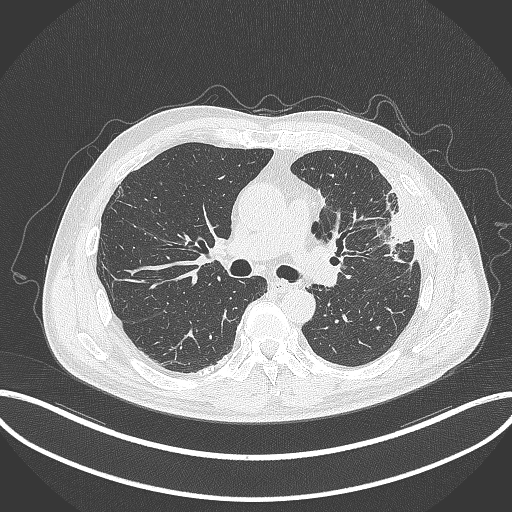
Chest CT, one axial slice. Slice 201 of 382 in the series (ordered by position). Reconstruction kernel B70f. 120 kVp. Lung window (W 1500 / L -600 HU). 1 mm slice thickness. 512 × 512 image matrix, field of view 415 × 415 mm. Male patient, age 64 years. From the clinical record (not read from this slice): clinical TNM (as recorded): T4 N1 M0; histopathological grade: G3.
Structures marked on this image (bounding box drawn by a radiologist):
- lung tumour (recorded histology: adenocarcinoma): bounding box <375,186,415,264> (left, top, right, bottom; pixels)